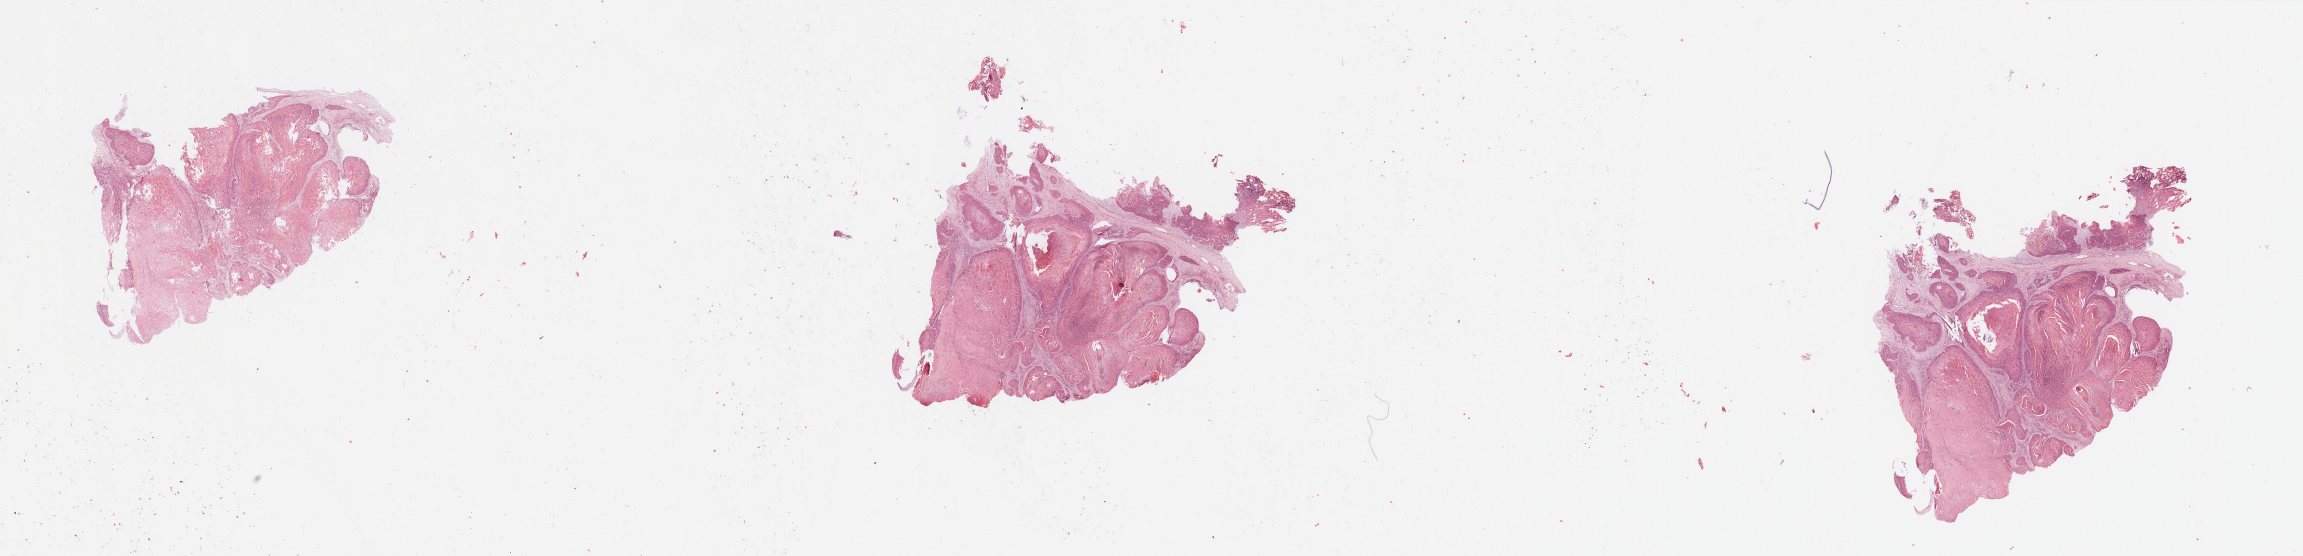
Hematoxylin and eosin (H&E) stained whole-slide image — whole scanned area (about 36.4 x 8.8 mm) shown as a low-resolution overview. Tumour tissue sample, sampled site: larynx. 71-year-old male patient. Histologic grade: G2 (moderately differentiated). Pathologist review of this section (percent, as recorded): tumour nuclei 85%, necrosis 2%.
• diagnosis: Squamous cell carcinoma, NOS (larynx, NOS)
• primary tumour site (as recorded): larynx
• AJCC pathologic stage: IVA